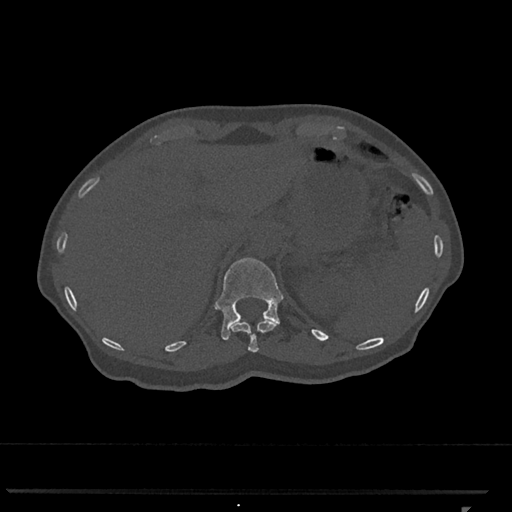
CT including the spine, one axial slice. Position 485 of 793 along the scan axis. Reconstruction kernel Br40s/3. Bone window (W 1800 / L 400 HU). 512 × 512 image matrix. Patient: female, 62 years. Case-level facts recorded for this patient, not image findings: primary cancer: renal.
Outlined on this slice (semi-automatic segmentation, software-assisted and operator-edited):
- T11 vertebra: bounding box <231,319,277,352> (left, top, right, bottom; pixels)
- T12 vertebra: <214,258,284,340>